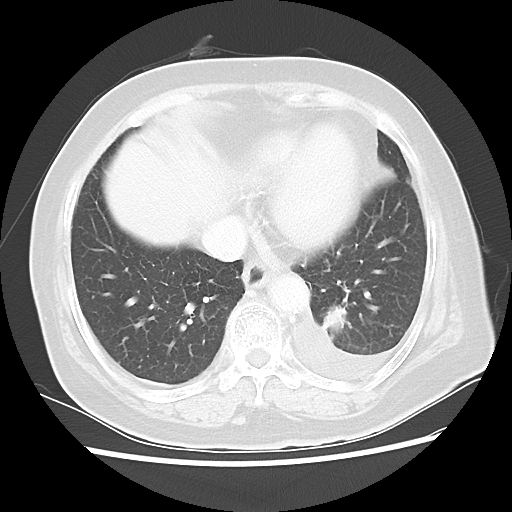
Chest CT, one axial slice; slice 10 of 40 in the series (ordered by position); reconstruction kernel LUNG; 100 kVp; lung window (W 1500 / L -600 HU); 512 × 512 image matrix, field of view 343 × 343 mm. Female patient, age 68 years. From the clinical record (not read from this slice): clinical TNM (as recorded): T1c N0 M1.
Annotated regions visible in this slice (rectangle marked by the reading radiologist):
- lung tumour (recorded histology: adenocarcinoma): bounding box [x1, y1, x2, y2] px = [317, 303, 353, 342]